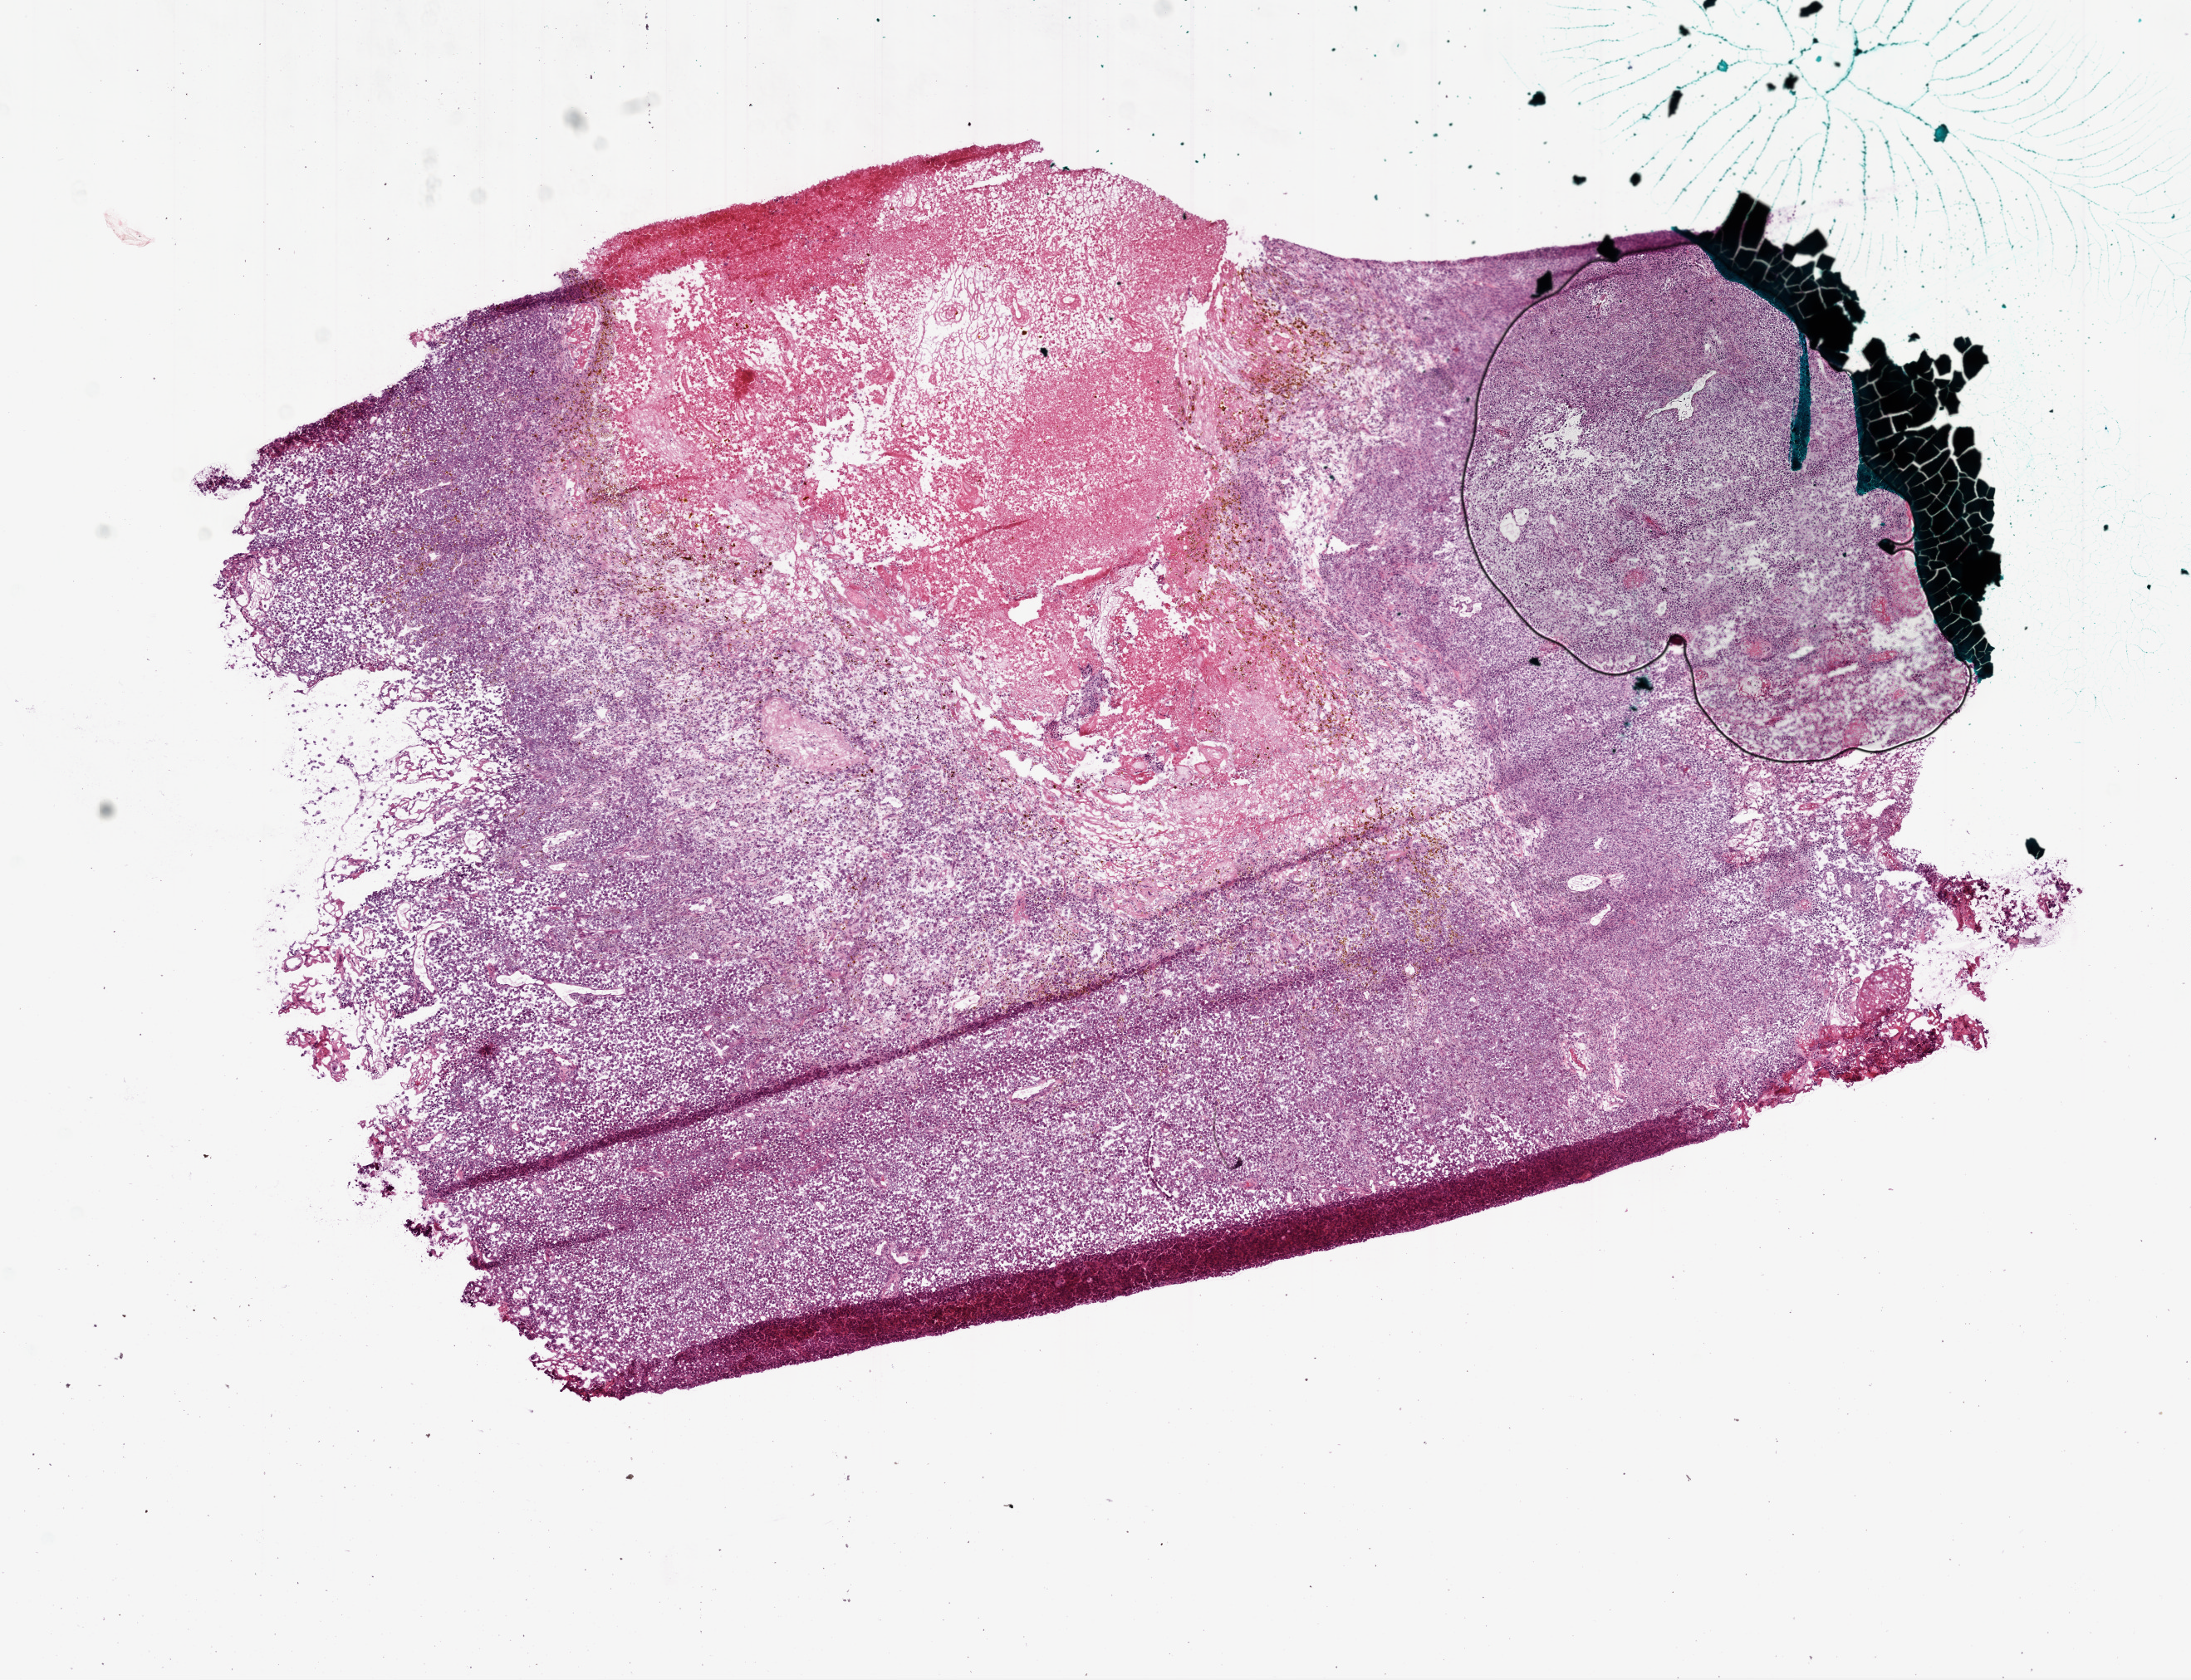
Whole-slide histology image, Hematoxylin and eosin (H&E) stained, shown as a low-resolution overview of the whole scanned area (about 10.6 x 8.2 mm, slide scanned at 20x). Frozen section from the bottom of the tissue portion. Primary tumour sample from the brain. Male, age 61 years at initial diagnosis. Pathologist review of this section (percent, as recorded): tumour cells 45%, tumour nuclei 85%, normal cells 0%, stromal cells 10%, necrosis 45%.
Diagnosis: Glioblastoma.